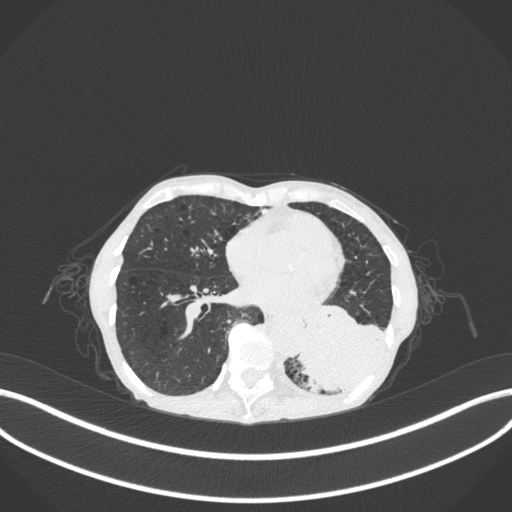
Chest CT, one axial slice. Slice 99 of 347 in the series (ordered by position). 120 kVp. Lung window (W 1500 / L -600 HU). 1 mm slice thickness. 512 × 512 image matrix, field of view 400 × 400 mm. Patient: female, 70 years. Case-level facts recorded for this patient, not image findings: clinical TNM (as recorded): T3 N0 M0.
Outlined on this slice (bounding box drawn by a radiologist):
- lung tumour (recorded histology: small cell carcinoma): box from (x=295, y=293) to (x=391, y=397) px